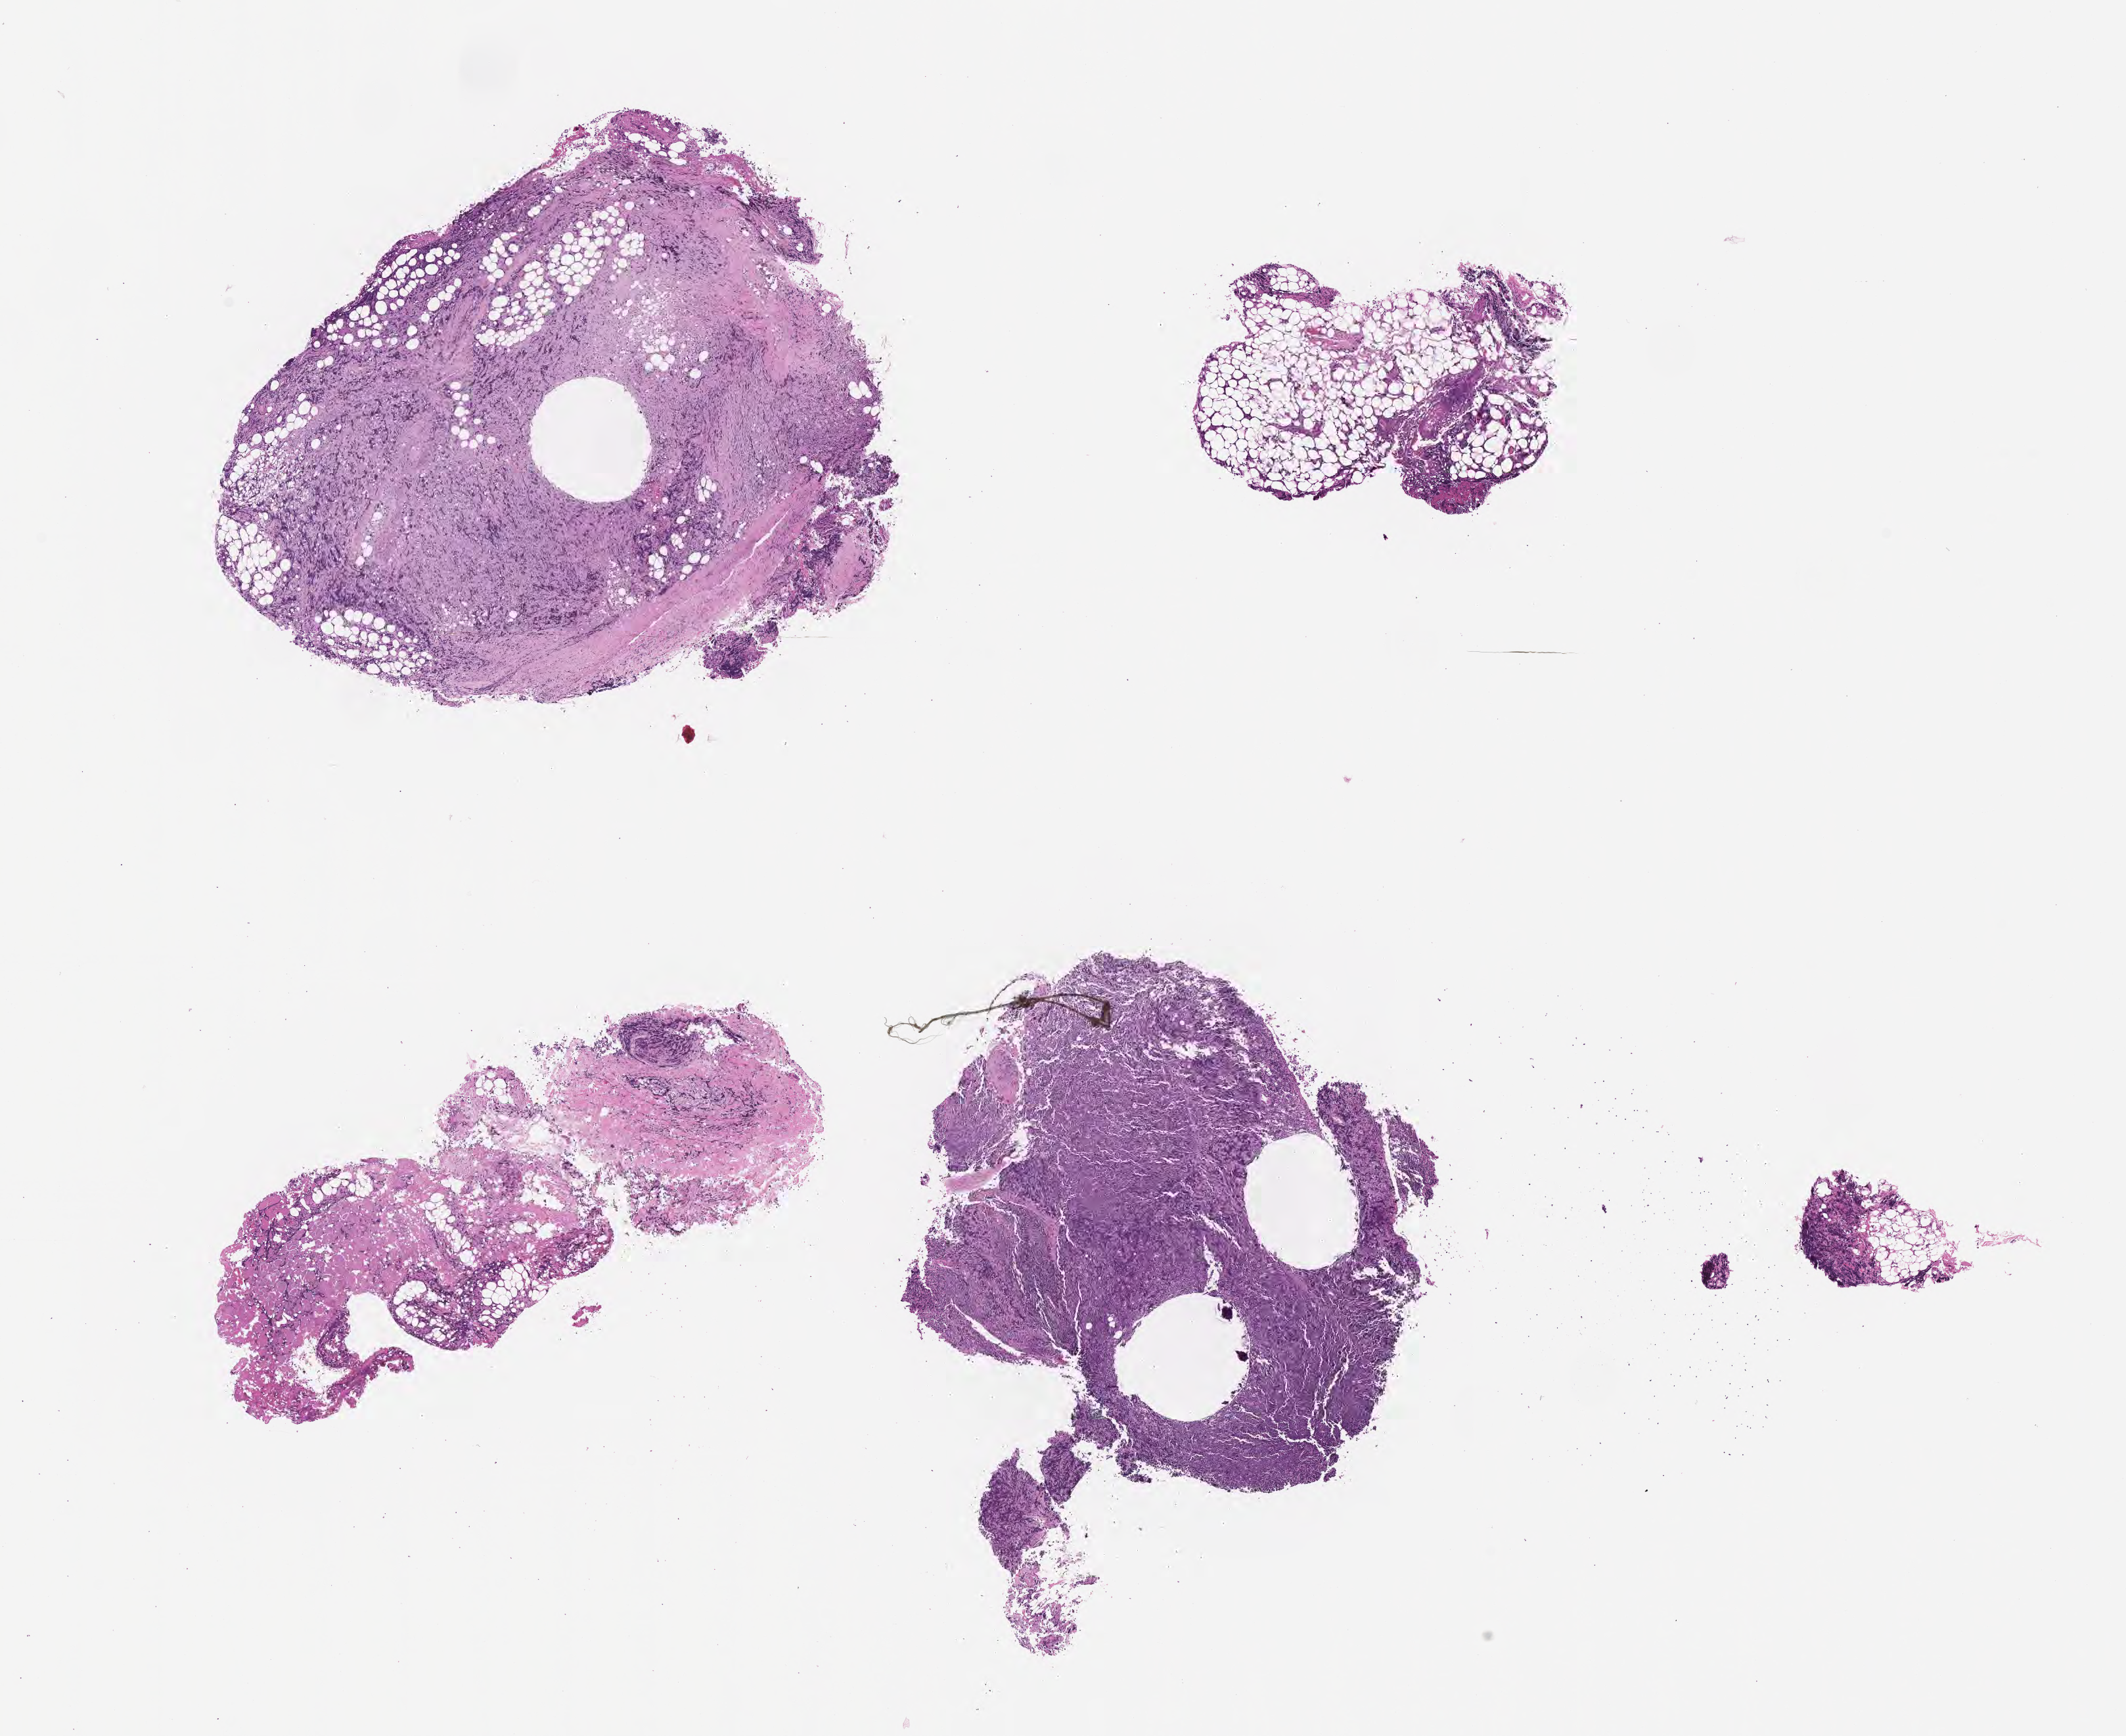
Whole-slide image, haematoxylin and eosin stain — shown as a low-resolution overview of the whole scanned area (about 13.1 x 10.7 mm), FFPE section, primary tumor. Patient: male, 54 years old. Pathologist review of this section (percent, as recorded): tumor cells 65%, tumor nuclei 90%.
Diagnosis: Burkitt lymphoma, NOS.